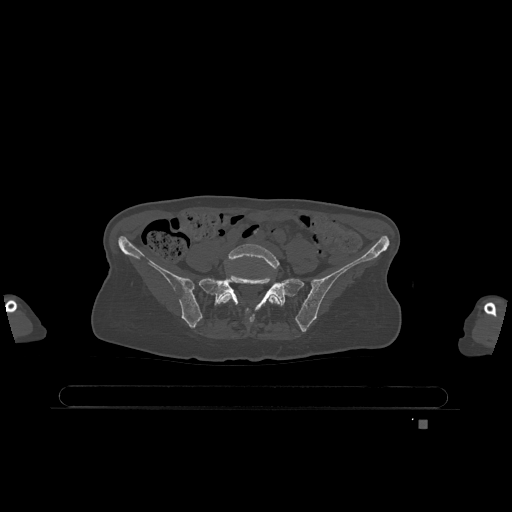
CT including the spine, one axial slice; position 212 of 1317 along the scan axis; bone window (W 1800 / L 400 HU); 0.5 mm slice thickness; 512 × 512 image matrix. Female patient, age 74 years. Case-level facts recorded for this patient, not image findings: primary cancer: lung.
Annotated regions visible in this slice (semi-automatically segmented with operator editing):
- L5 vertebra: box from (x=218, y=244) to (x=282, y=314) px